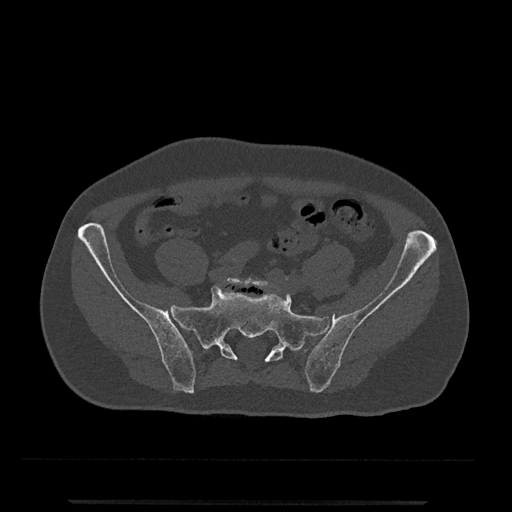
CT including the spine, one axial slice. Reconstruction kernel Br40s/3. Bone window (W 1800 / L 400 HU). 0.5 mm slice thickness. 512 × 512 image matrix, field of view 419 × 419 mm. Patient: male, 63 years. From the clinical record (not read from this slice): primary cancer: prostate.
Annotated regions visible in this slice (semi-automatic segmentation, software-assisted and operator-edited):
- L5 vertebra: bounding box <222,277,271,288> (left, top, right, bottom; pixels)